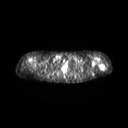
FDG PET of an extremity soft-tissue mass (from a PET/CT study), one axial slice. Slice 211 of 267 in the series (ordered by position). 3.27 mm slice thickness. 128 × 128 image matrix, field of view 600 × 600 mm. Patient: female, 28 years. From the clinical record (not read from this slice): histological type: malignant fibrous histiocytoma; grade: low; site of the primary tumour: left arm.
Annotated regions visible in this slice (expert contour drawn on MRI and transferred to this co-registered scan by the dataset authors):
- gross tumour volume (mass): bounding box <99,63,105,70> (left, top, right, bottom; pixels)